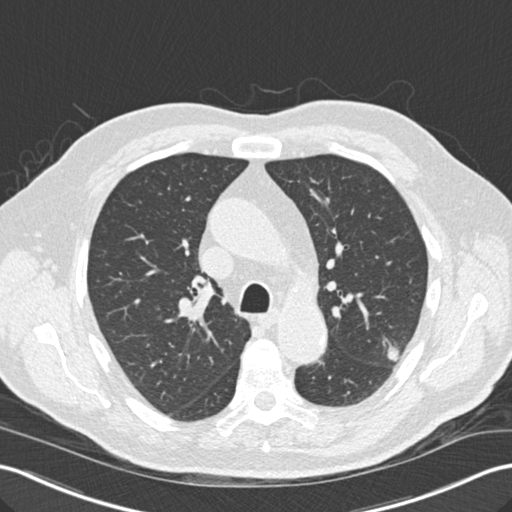
Axial slice from a low-dose chest CT screening exam, third annual screen, lung window (W 1500 / L -600 HU), slice 56 of 157 in the series, 512 × 512 image matrix. Male, age 67 years at enrolment. Former smoker at enrolment.
Expert reader's lesion annotation, bounding box (x1, y1, x2, y2) in pixels: (365, 329, 415, 376). The screening reader recorded 2 non-calcified nodules or masses ≥4 mm on this exam (left upper lobe, left lower lobe); which of them this box marks is not recorded. Later outcome: lung cancer diagnosed 55 days after this screen — squamous cell carcinoma, large cell, nonkeratinizing, NOS, left upper lobe, moderately differentiated (G2), stage IA (AJCC 6th edition), 15 mm at pathology.